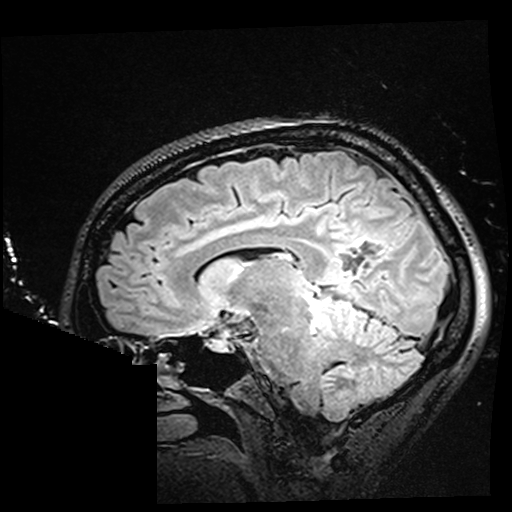
Brain MRI from a brain-tumour surgery series, one sagittal slice; position 100 of 176 along the scan axis; T2 FLAIR; 1 mm slice thickness; 512 × 512 image matrix, field of view 250 × 250 mm. Case-level facts recorded for this patient, not image findings: histopathology: Oligodendroglioma; WHO grade: 2; IDH mutation: yes; tumour location: Right Parietal.
Annotated regions visible in this slice (outlined manually by an expert reader):
- residual tumour: box from (x=325, y=279) to (x=349, y=291) px